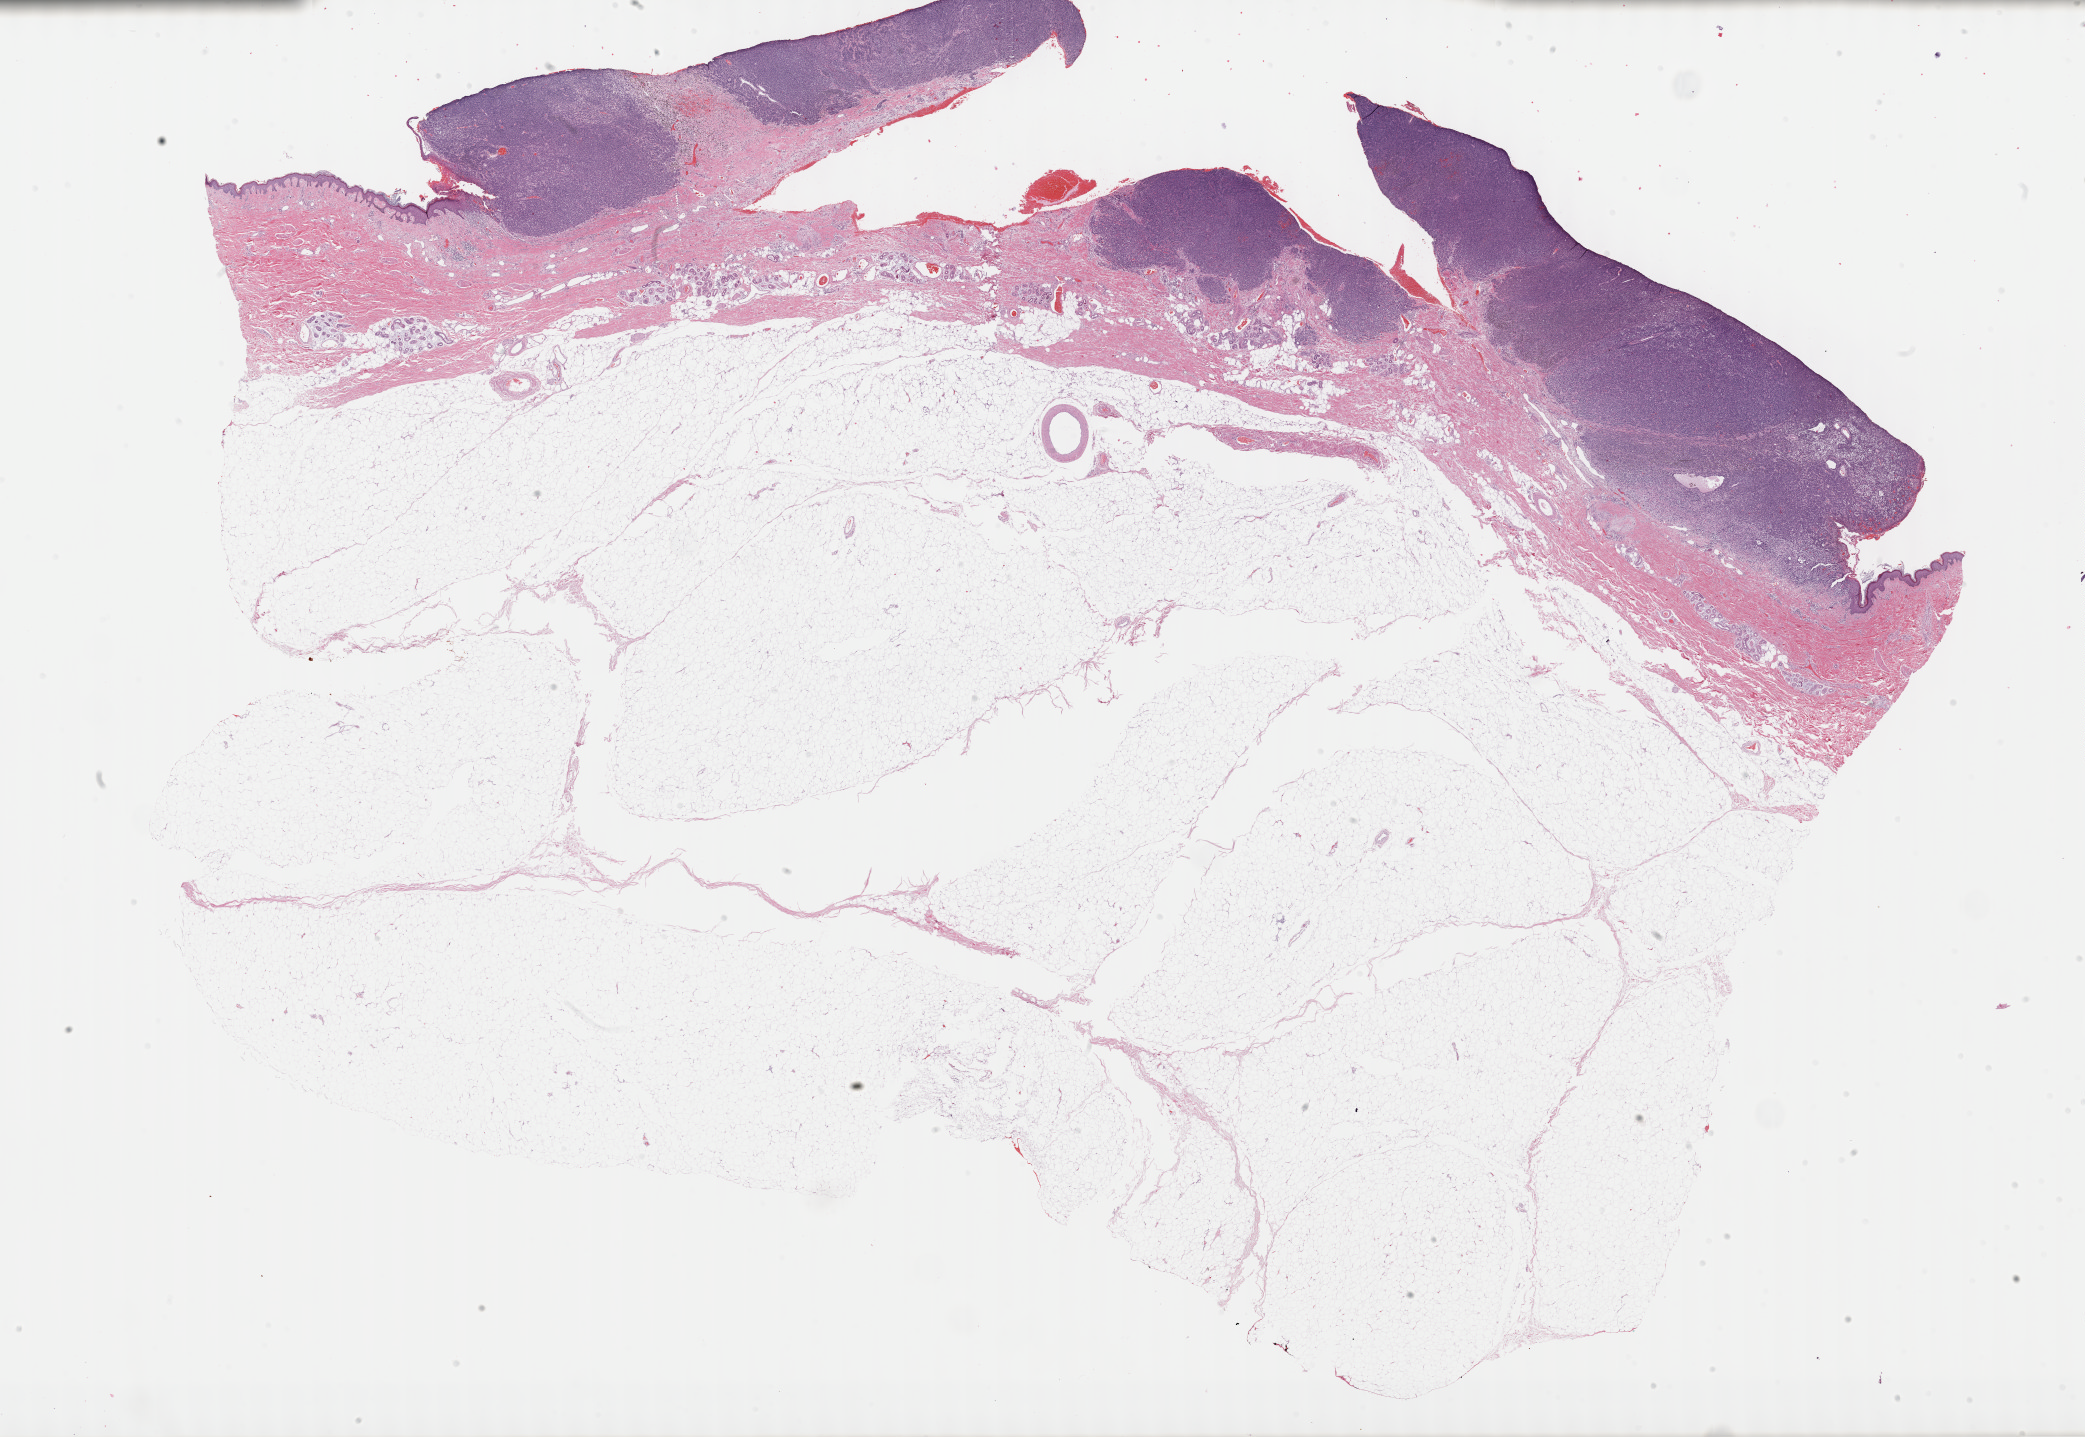
Digitized H&E tissue section (whole slide) — a low-resolution overview of the entire scanned area, about 33.7 x 23.2 mm. Formalin-fixed paraffin-embedded (FFPE) diagnostic section. Skin, primary tumour sample. Male, age 68 years at initial diagnosis.
Diagnosis: Malignant melanoma, NOS.